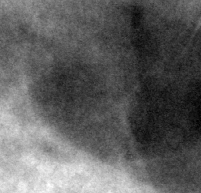
Region of interest cut from a scanned film mammogram (one marked finding); left breast; MLO view; BI-RADS breast density category 2 (scale 1–4).
- Calcifications, morphology pleomorphic, distribution clustered; BI-RADS assessment category 4; pathology (as recorded): benign.